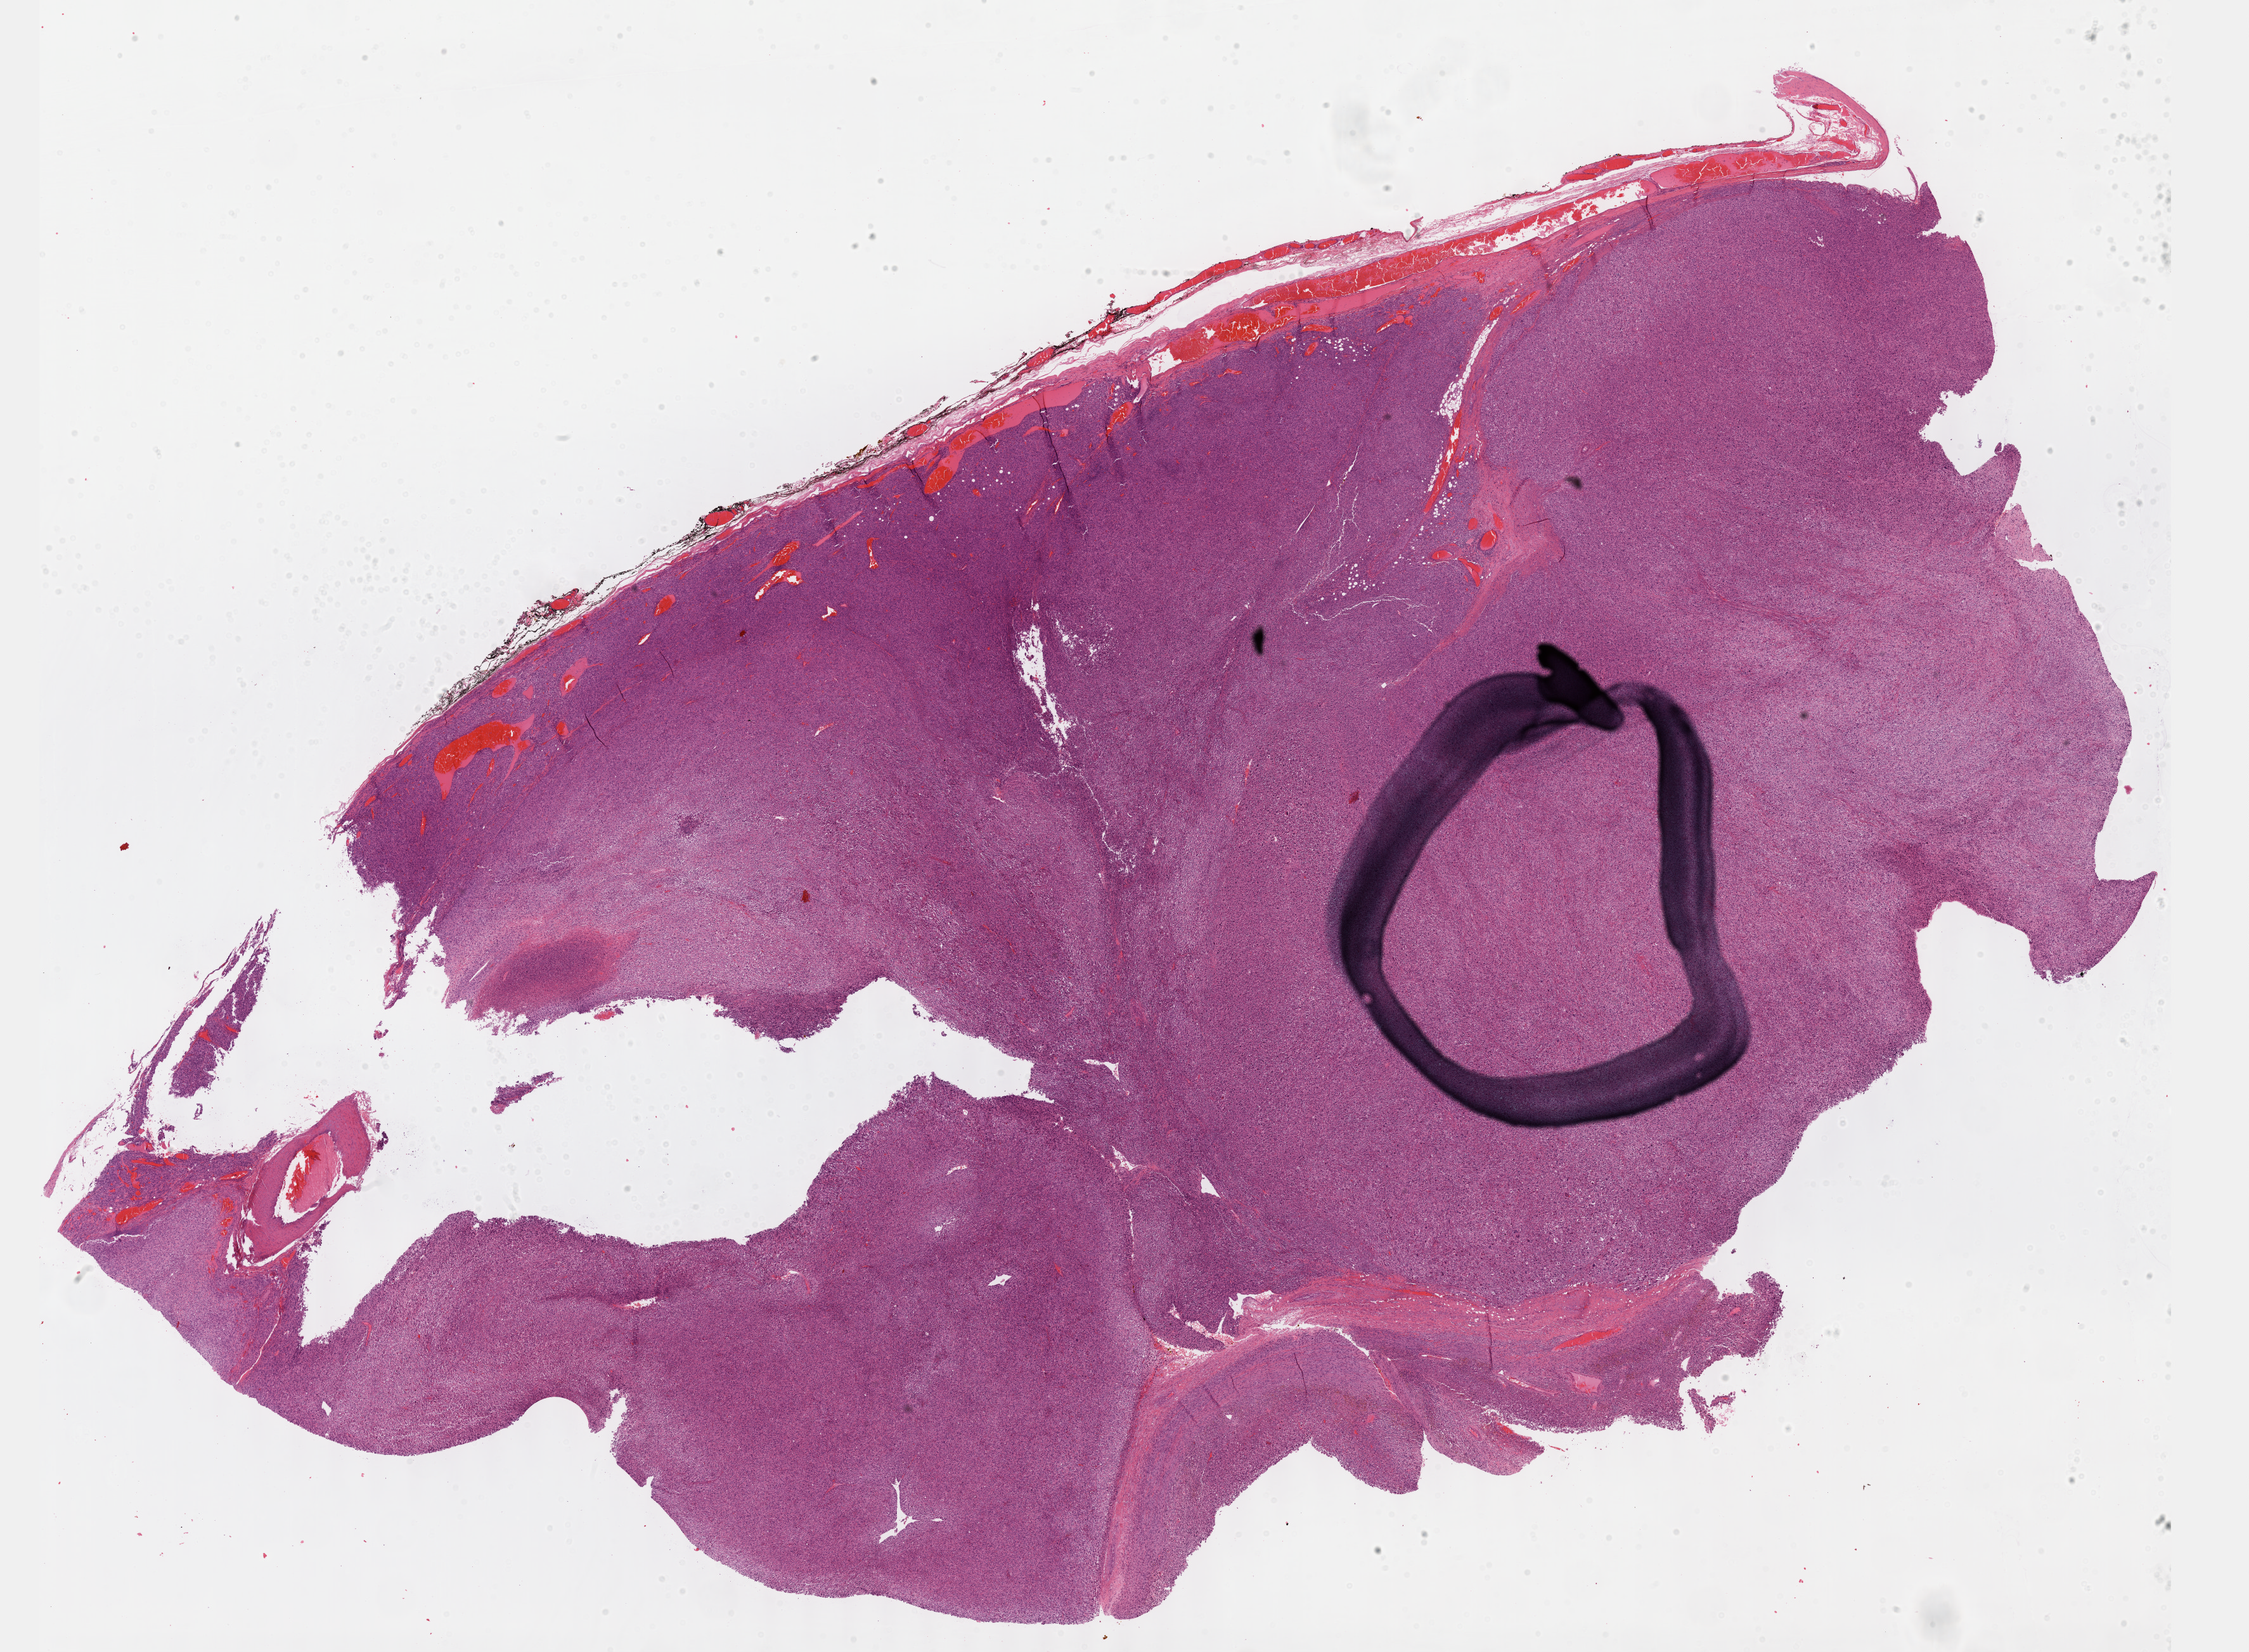
Whole-slide histology image, H&E — low-resolution overview of the scanned area, about 28.7 x 21.1 mm (slide scanned at 40x), formalin-fixed paraffin-embedded (FFPE) diagnostic section, sample: primary tumour, connective, subcutaneous and other soft tissues. Male, age 29 years at initial diagnosis.
• pathologic diagnosis: Malignant peripheral nerve sheath tumor (connective, subcutaneous and other soft tissues of lower limb and hip)